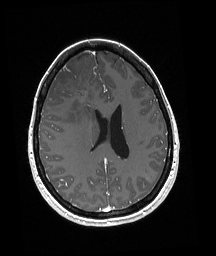
Brain MRI from a brain-tumour surgery series, one axial slice; slice 78 of 192 in the series (ordered by position); T1-weighted post-contrast; 1 mm slice thickness; 216 × 256 image matrix, field of view 211 × 250 mm. Case-level facts recorded for this patient, not image findings: histopathology: Oligodendroglioma; WHO grade: 3; IDH mutation: yes; tumour location: Right Frontal.
Annotated regions visible in this slice (outlined manually by an expert reader):
- tumour: bounding box <59,82,86,92> (left, top, right, bottom; pixels)